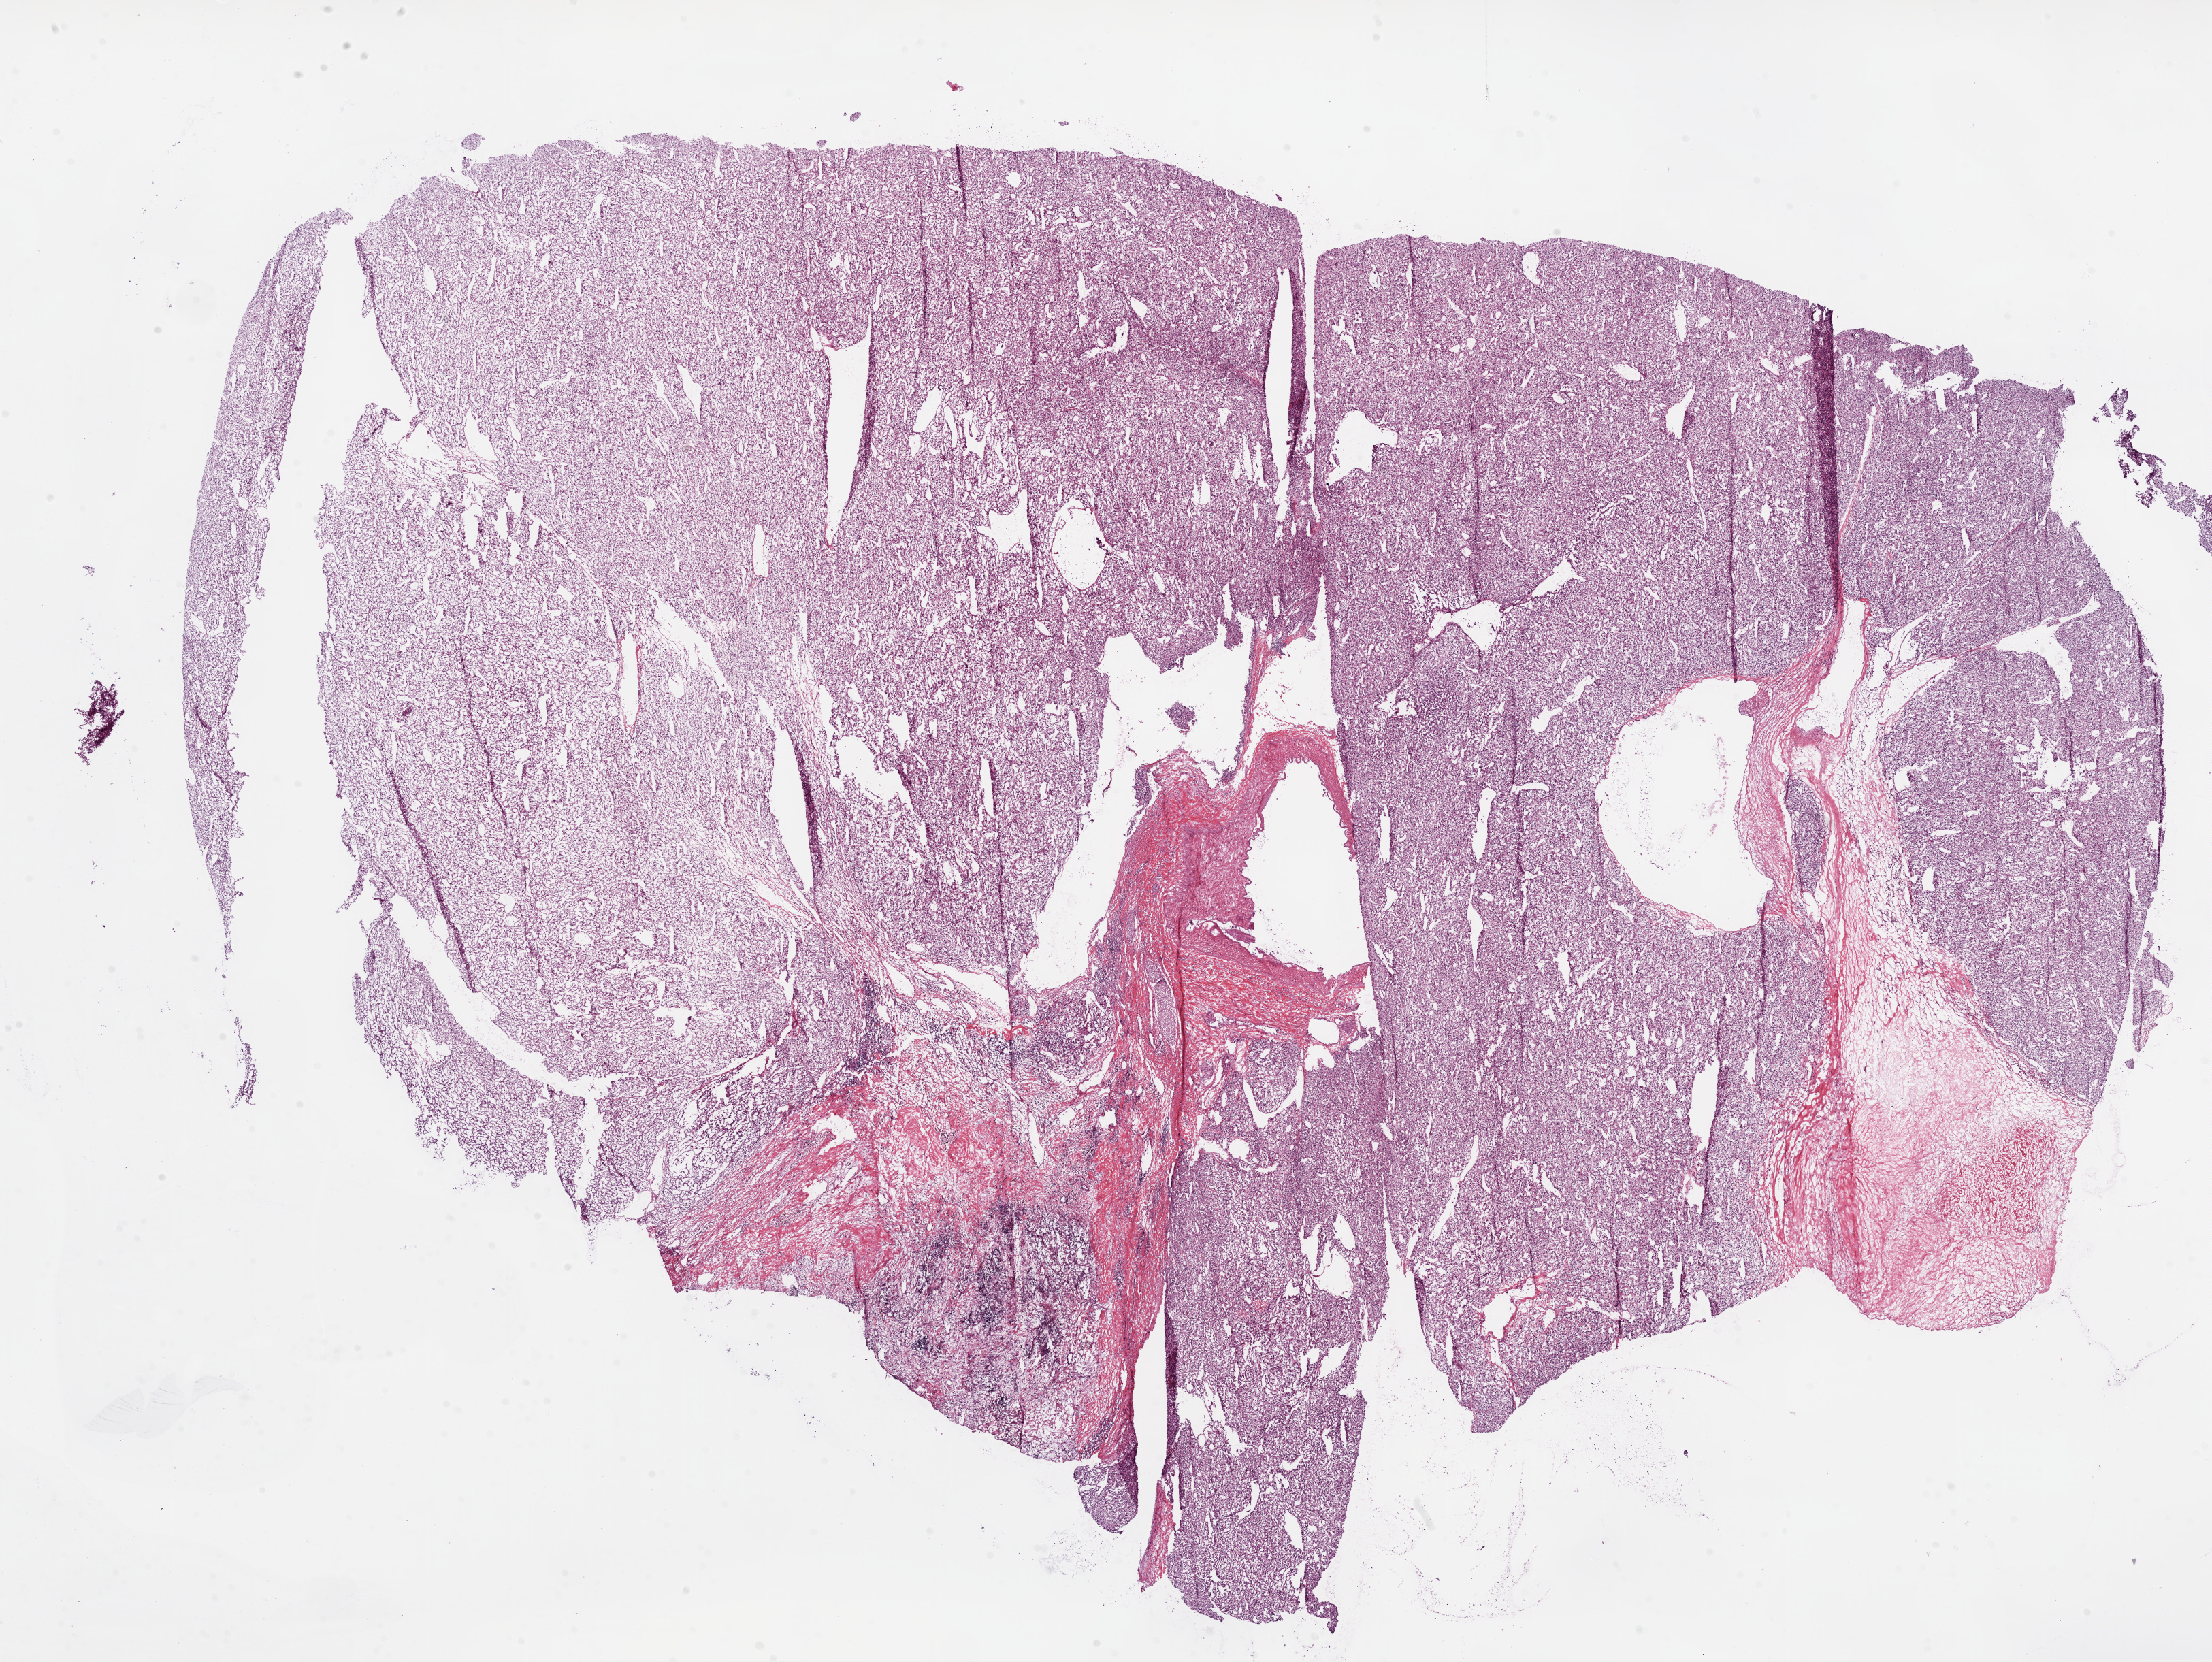
H&E-stained whole-slide image, whole scanned area (about 26.1 x 19.6 mm, slide scanned at 20x) shown as a low-resolution overview, frozen section, primary tumour sample from the kidney. Patient: male, age at initial diagnosis 58 years.
Diagnosis: Clear cell adenocarcinoma, NOS.